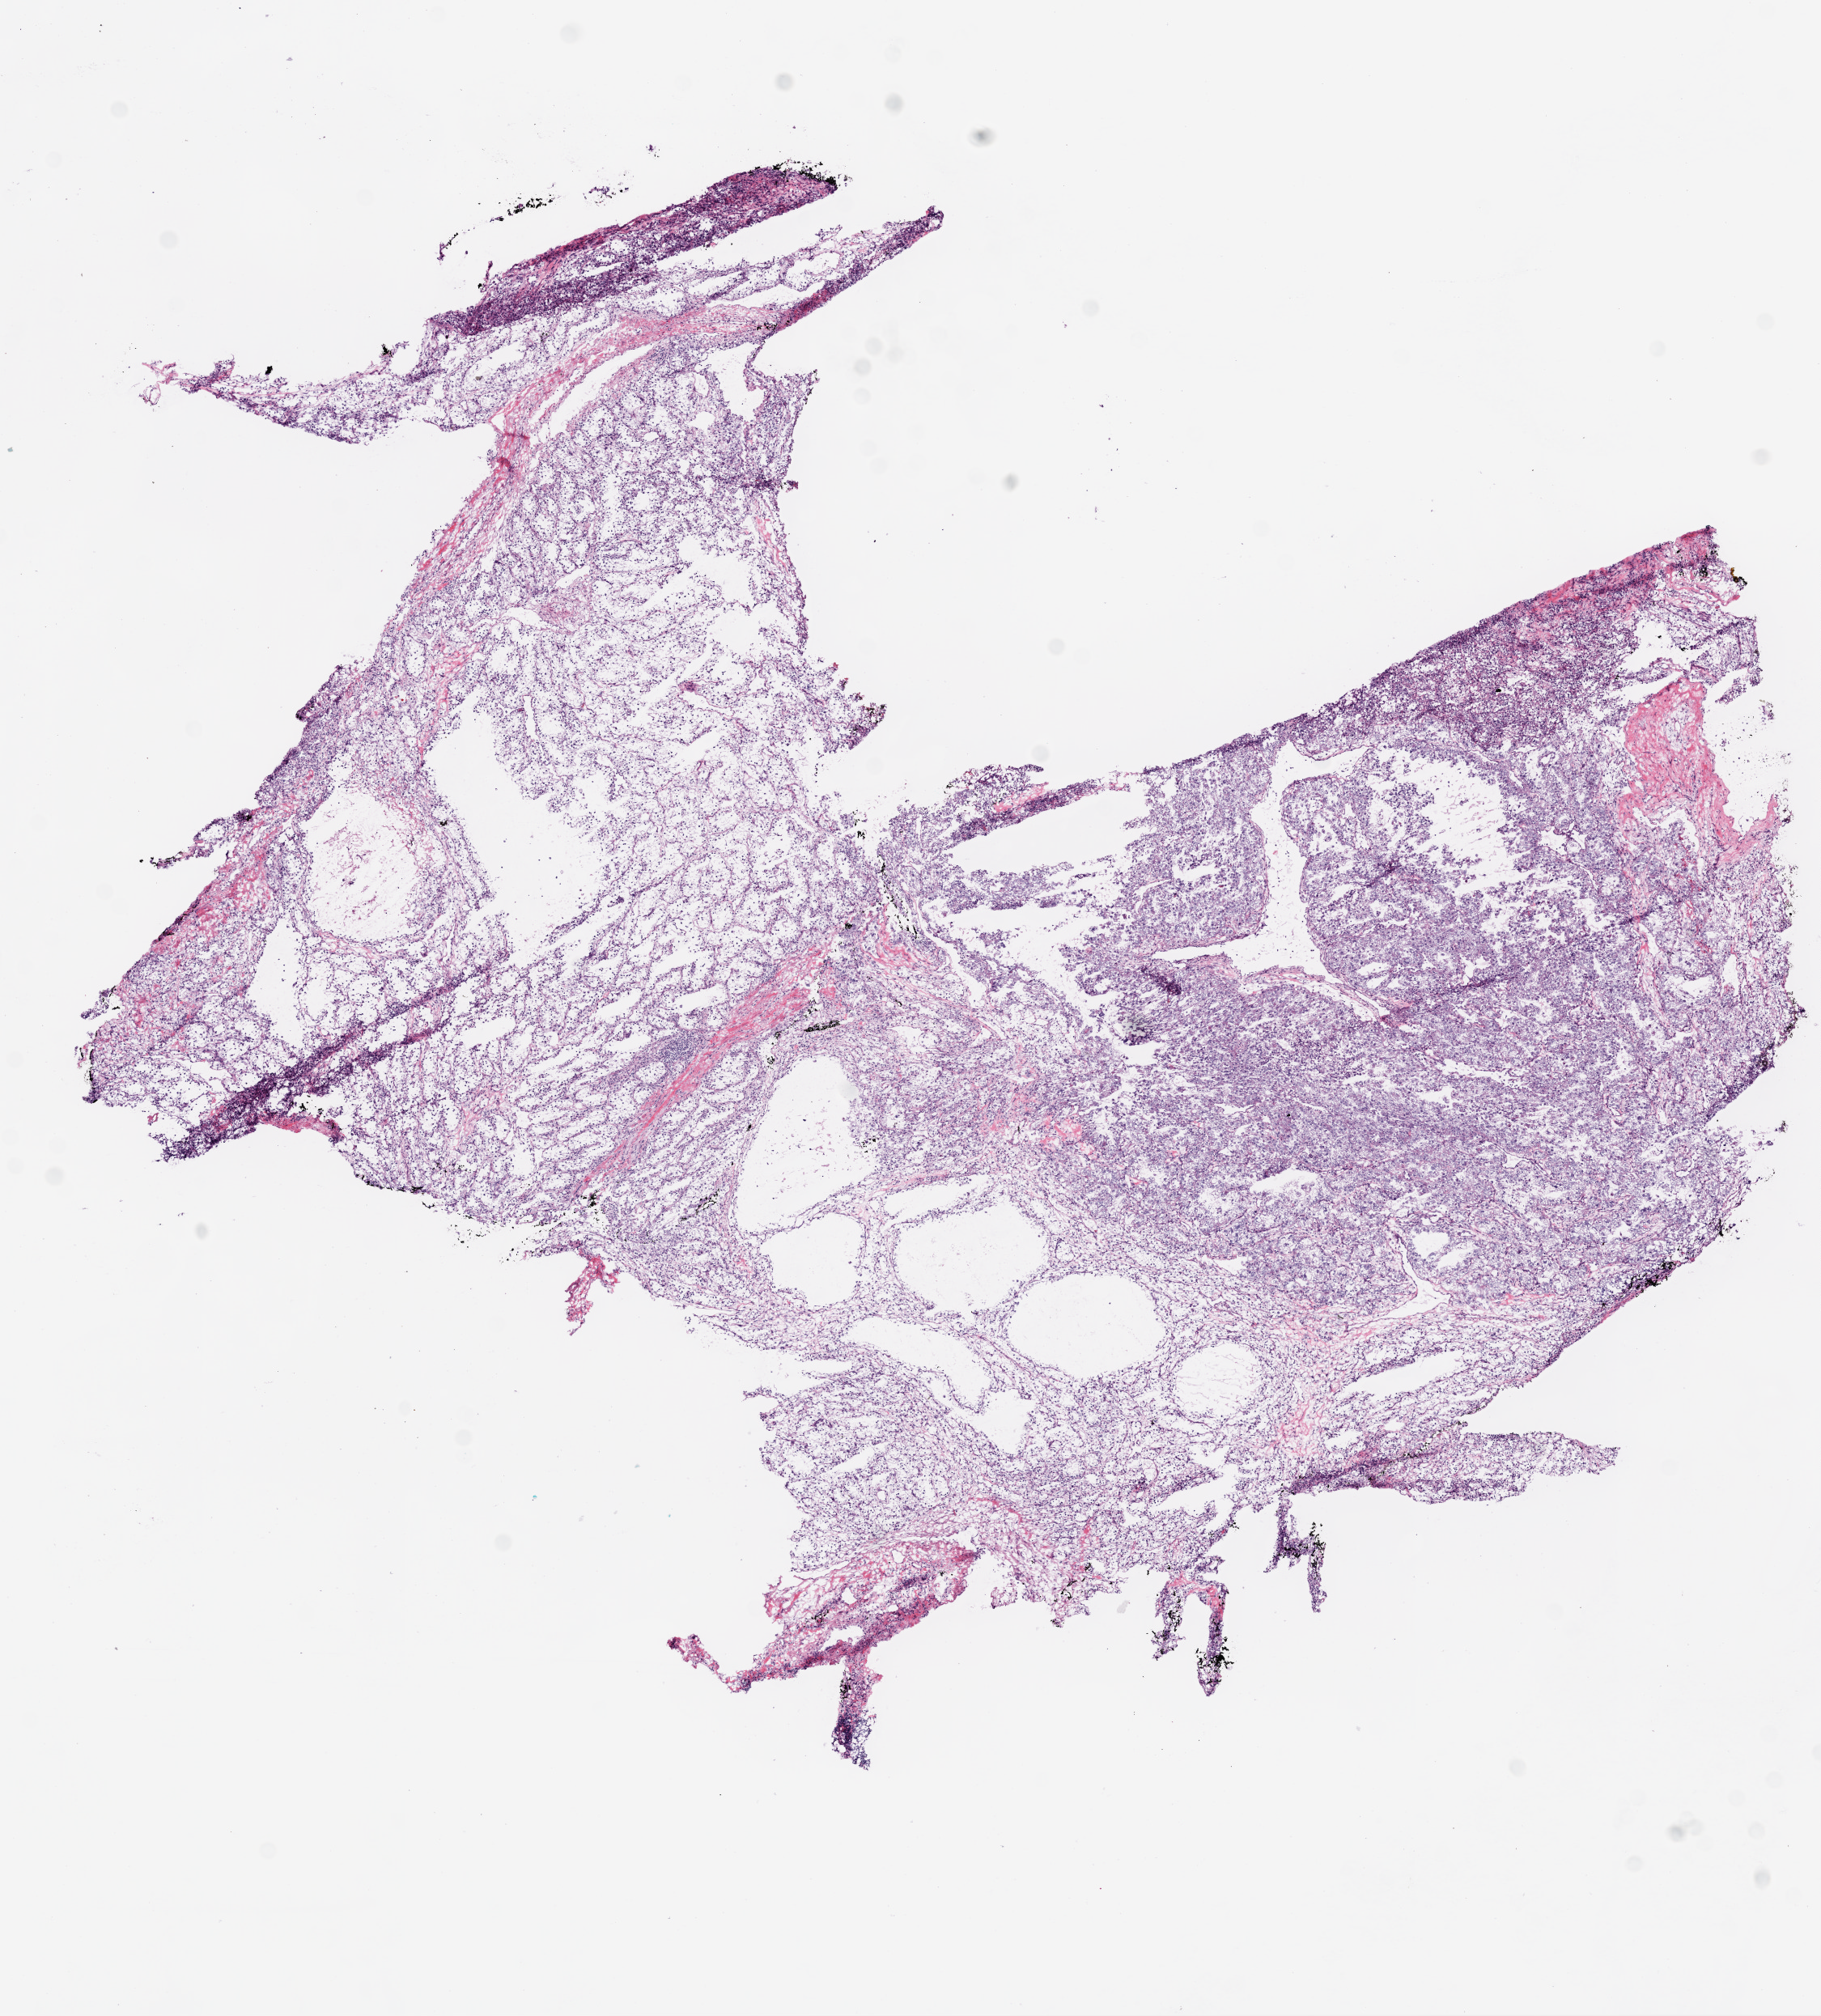
Whole-slide histology image, H&E-stained, a low-resolution overview of the entire scanned area, about 9.0 x 10.0 mm. Frozen section from the top of the tissue portion. Kidney, primary tumour sample. Female, age 77 years at initial diagnosis. Histologic grade: G2 (moderately differentiated). Slide review estimates, as recorded: tumour cells 90%, tumour nuclei 80%, normal cells 0%, stromal cells 10%, necrosis 0%.
Histologic diagnosis: Clear cell adenocarcinoma, NOS. AJCC pathologic stage: III. Laterality: right.